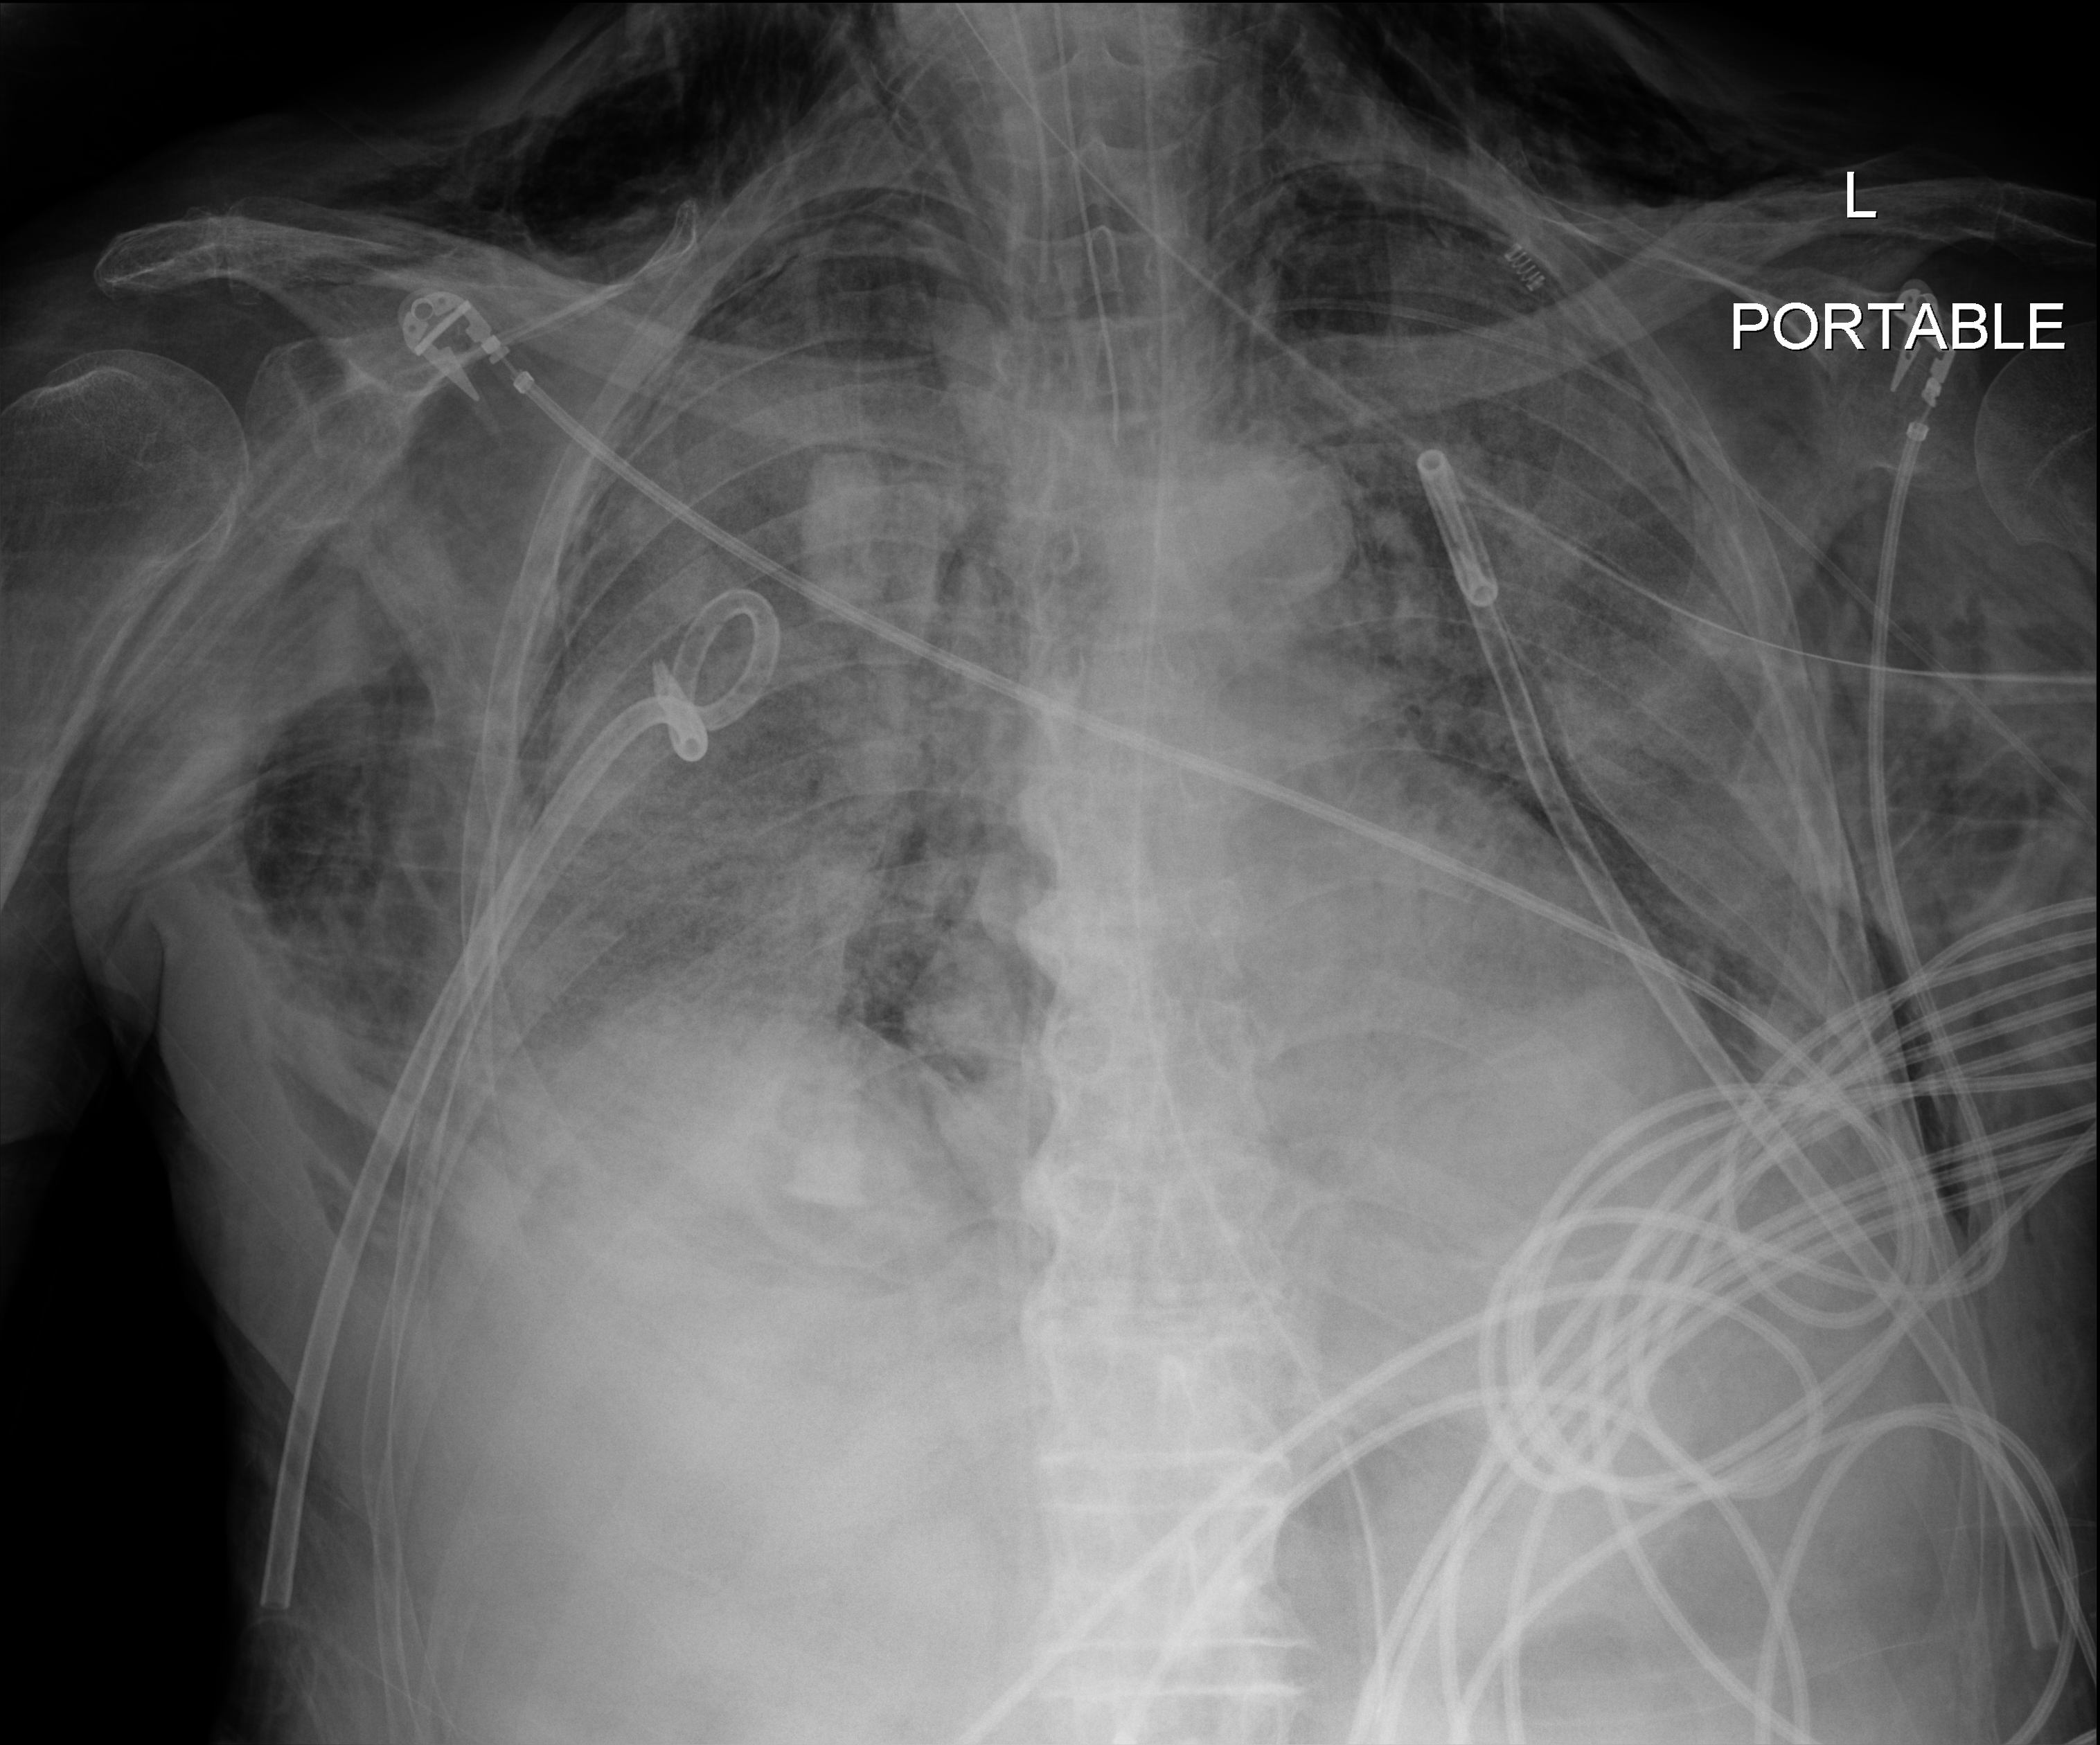
Bedside chest radiograph (digital radiography); anteroposterior (AP) projection. Patient hospitalised with COVID-19; male, aged 75–90 years.
Hospital-stay facts (about this admission, not read from this image; timing relative to this image not recorded): chronic kidney disease (admission record): no; mechanically ventilated during this hospital stay: yes.